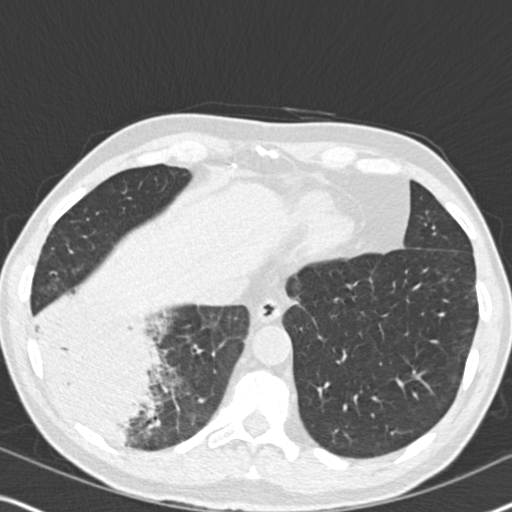
Low-dose screening chest CT, one axial slice; slice 57 of 182 in the series (ordered by position); 120 kVp; lung window (W 1500 / L -600 HU); 512 × 512 image matrix, field of view 330 × 330 mm.
Outlined on this slice (expert manual segmentation):
- lesion 1 (tumor, lower lobe of right lung): box from (x=40, y=311) to (x=155, y=441) px